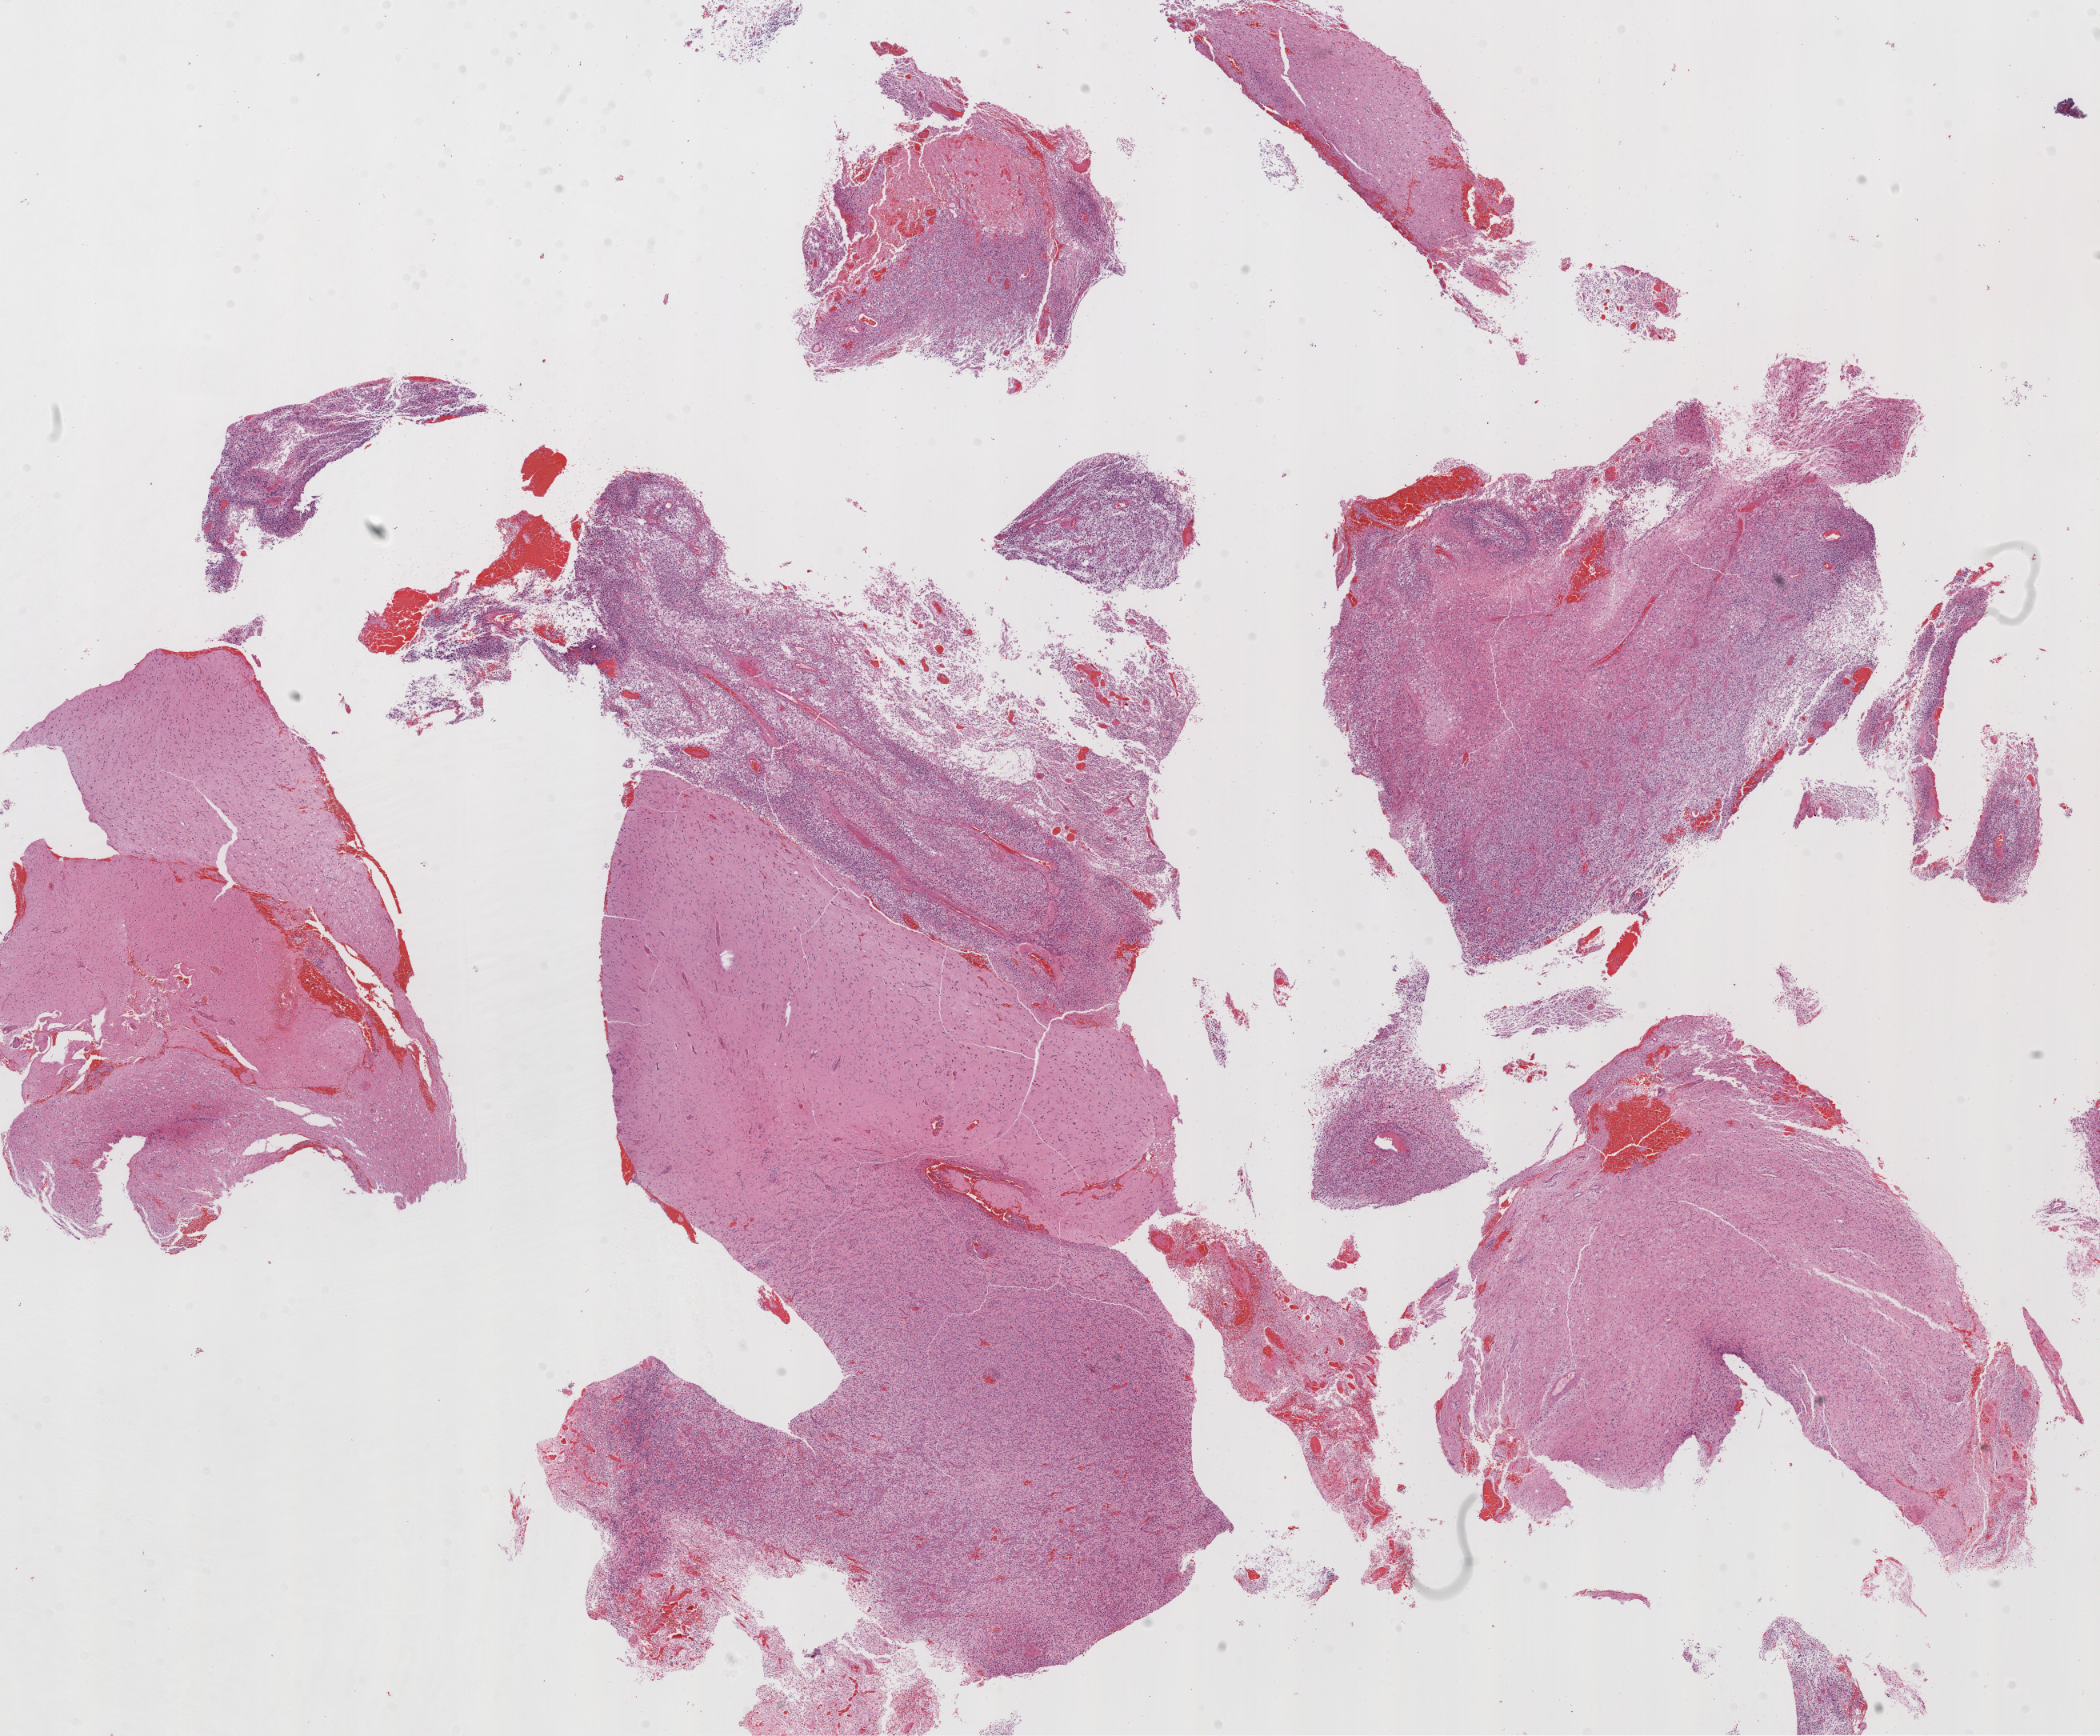
Digitized H&E tissue section (whole slide), shown as a low-resolution overview of the whole scanned area (about 21.1 x 17.4 mm, from a 20x scan). FFPE section. Primary tumour sample from the brain. Male, age 54 years at initial diagnosis.
Diagnosis: Glioblastoma.